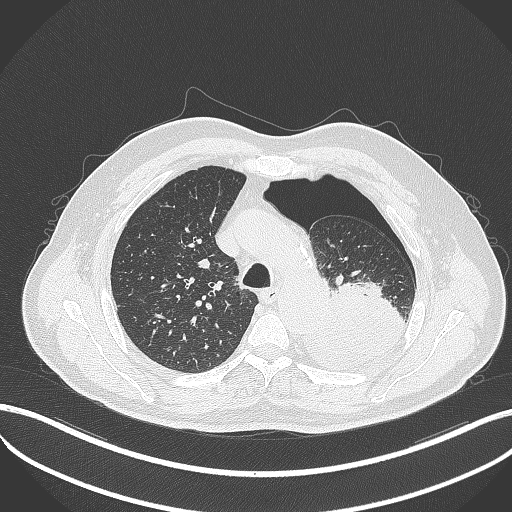
Chest CT, one axial slice. Slice 375 of 464 in the series (ordered by position). Reconstruction kernel B70f. 120 kVp. Lung window (W 1500 / L -600 HU). 512 × 512 image matrix. Male patient, age 76 years. Case-level facts recorded for this patient, not image findings: clinical TNM (as recorded): T3 N0 M1b.
Annotated regions visible in this slice (bounding box drawn by a radiologist):
- lung tumour (recorded histology: adenocarcinoma): bounding box [x1, y1, x2, y2] px = [299, 279, 410, 374]